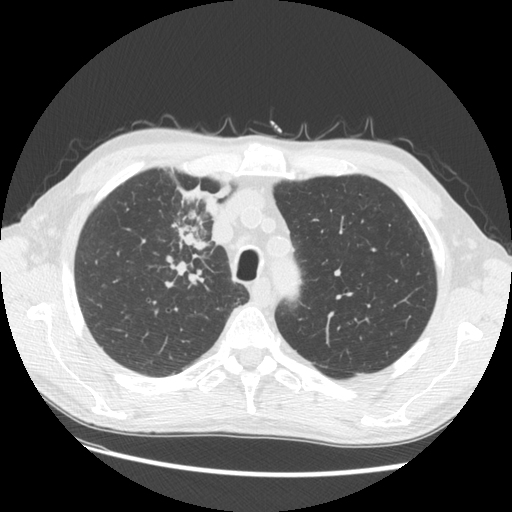
Axial slice from a low-dose chest CT screening exam, third screening round (two years after baseline), lung window (W 1500 / L -600 HU), 120 kVp, slice 29 of 133 in the series. Male, age 73 years at enrolment.
Expert reader's lesion annotation, box from (x=142, y=181) to (x=232, y=281) px. The screening reader recorded 4 non-calcified nodules or masses ≥4 mm on this exam; which of them this box marks is not recorded. Official screen result: positive, other. Later outcome: lung cancer diagnosed 48 days after this screen — squamous cell carcinoma, NOS, right upper lobe, poorly differentiated (G3), stage IIIB (AJCC 6th edition), 56 mm at pathology.